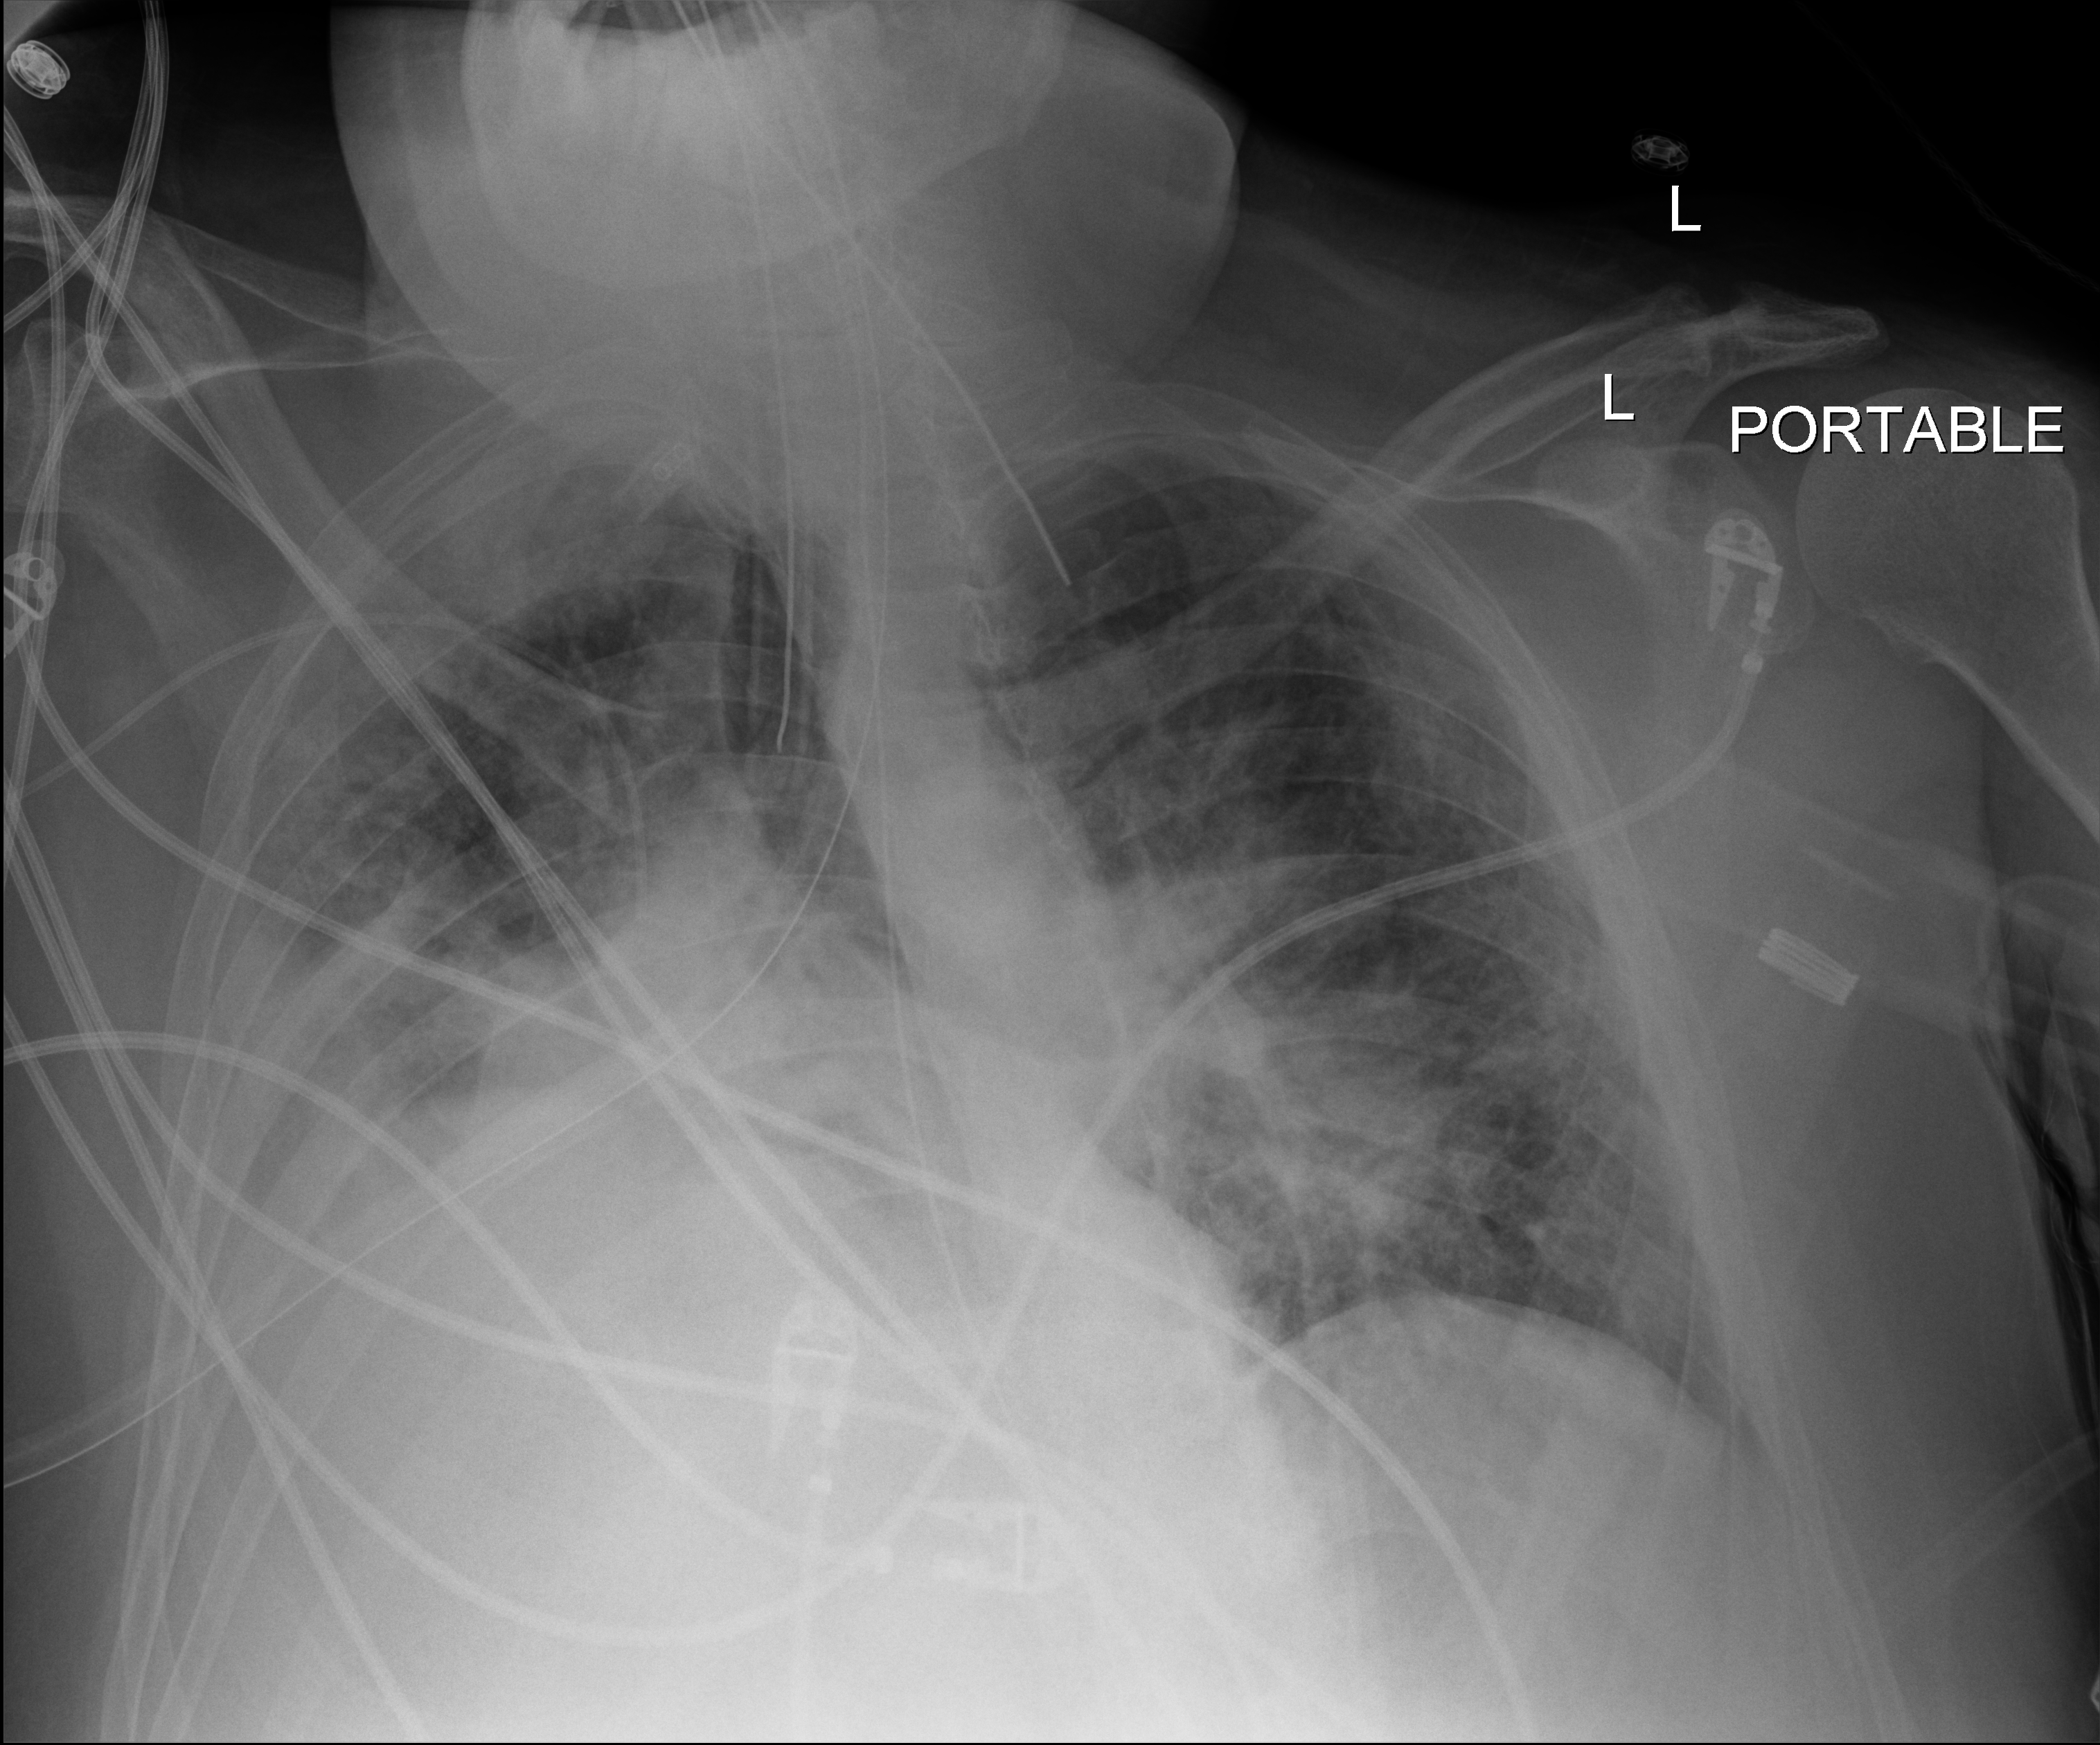
Portable chest radiograph; anteroposterior (AP) projection. Patient hospitalised with COVID-19, aged 18–59 years.
Admission-level facts for this patient (not findings on this image; timing relative to this image not recorded): mechanically ventilated during this hospital stay: yes; admitted to intensive care during this hospital stay: yes.